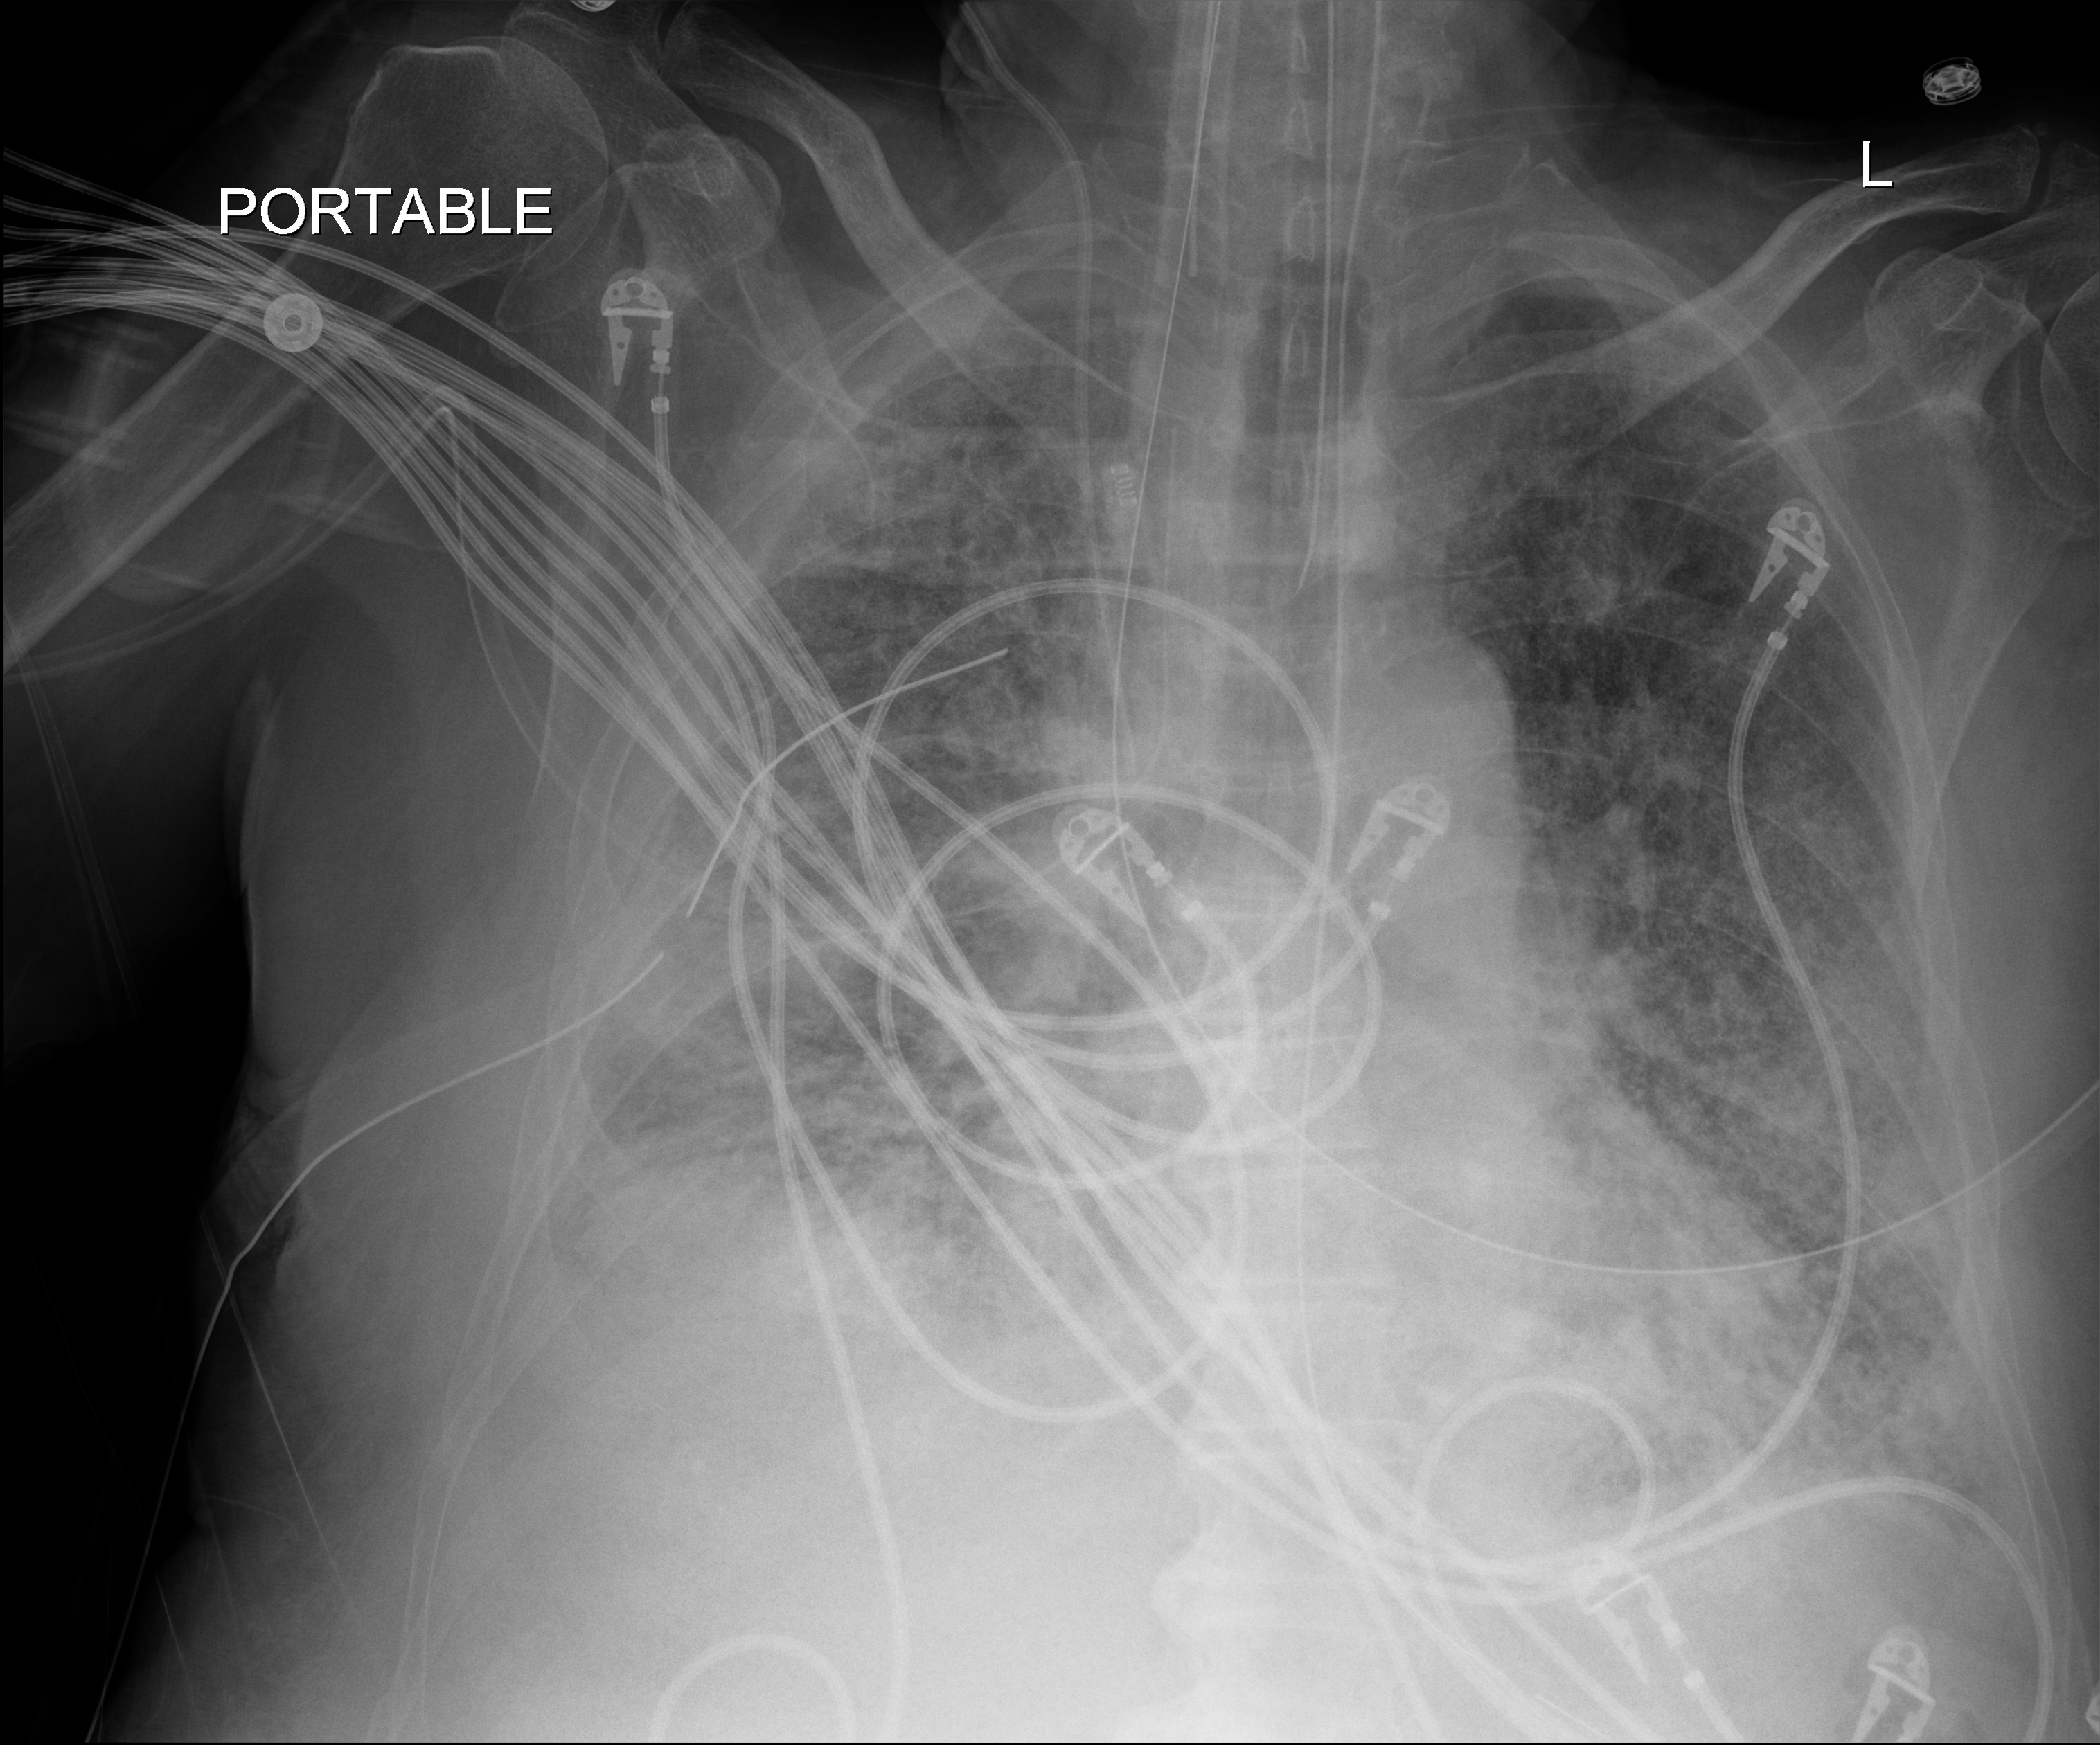
Portable chest radiograph; anteroposterior (AP) projection. Patient hospitalised with COVID-19; male, aged 75–90 years.
From the hospital-stay record, not from the radiograph (when in the stay this image was taken is not recorded):
- admitted to intensive care during this hospital stay: yes